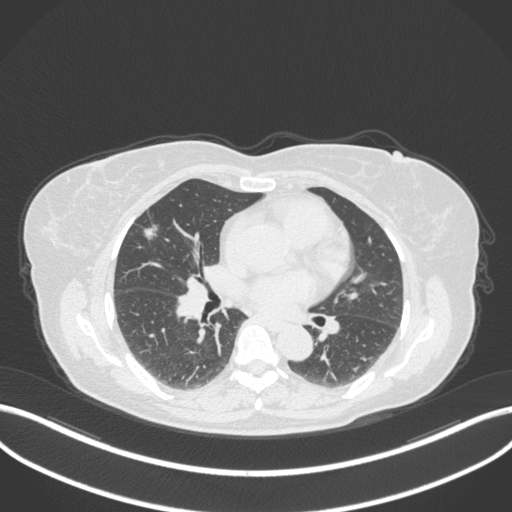
Chest CT, one axial slice. Slice 172 of 310 in the series (ordered by position). Lung window (W 1500 / L -600 HU). 1 mm slice thickness. 512 × 512 image matrix, field of view 400 × 400 mm. Patient: female, 55 years. Case-level facts recorded for this patient, not image findings: clinical TNM (as recorded): T1b N0 M0; histopathological grade: G2.
Annotated regions visible in this slice (bounding box drawn by a radiologist):
- lung tumour (recorded histology: adenocarcinoma): bounding box [x1, y1, x2, y2] px = [137, 218, 163, 244]